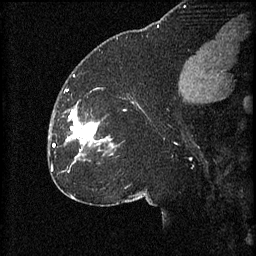
Breast MRI (dynamic contrast-enhanced), one sagittal slice; slice 30 of 60 in the series (ordered by position); 3 images stored at this slice position (order not interpretable as contrast timing); 1.5 T; TE 4.2 ms, TR 8.2 ms; 2 mm slice thickness; 256 × 256 image matrix, field of view 180 × 180 mm. Female patient, age 32 years.
Annotated regions visible in this slice (semi-automatic segmentation, software-assisted and operator-edited):
- analysis volume of interest (the breast-tissue region the enhancement analysis was run in; not a lesion): box from (x=65, y=106) to (x=111, y=163) px
- tumour enhancement mask (voxels above the 70 % enhancement threshold inside the analysis volume of interest): (x=66, y=110)–(x=102, y=145)